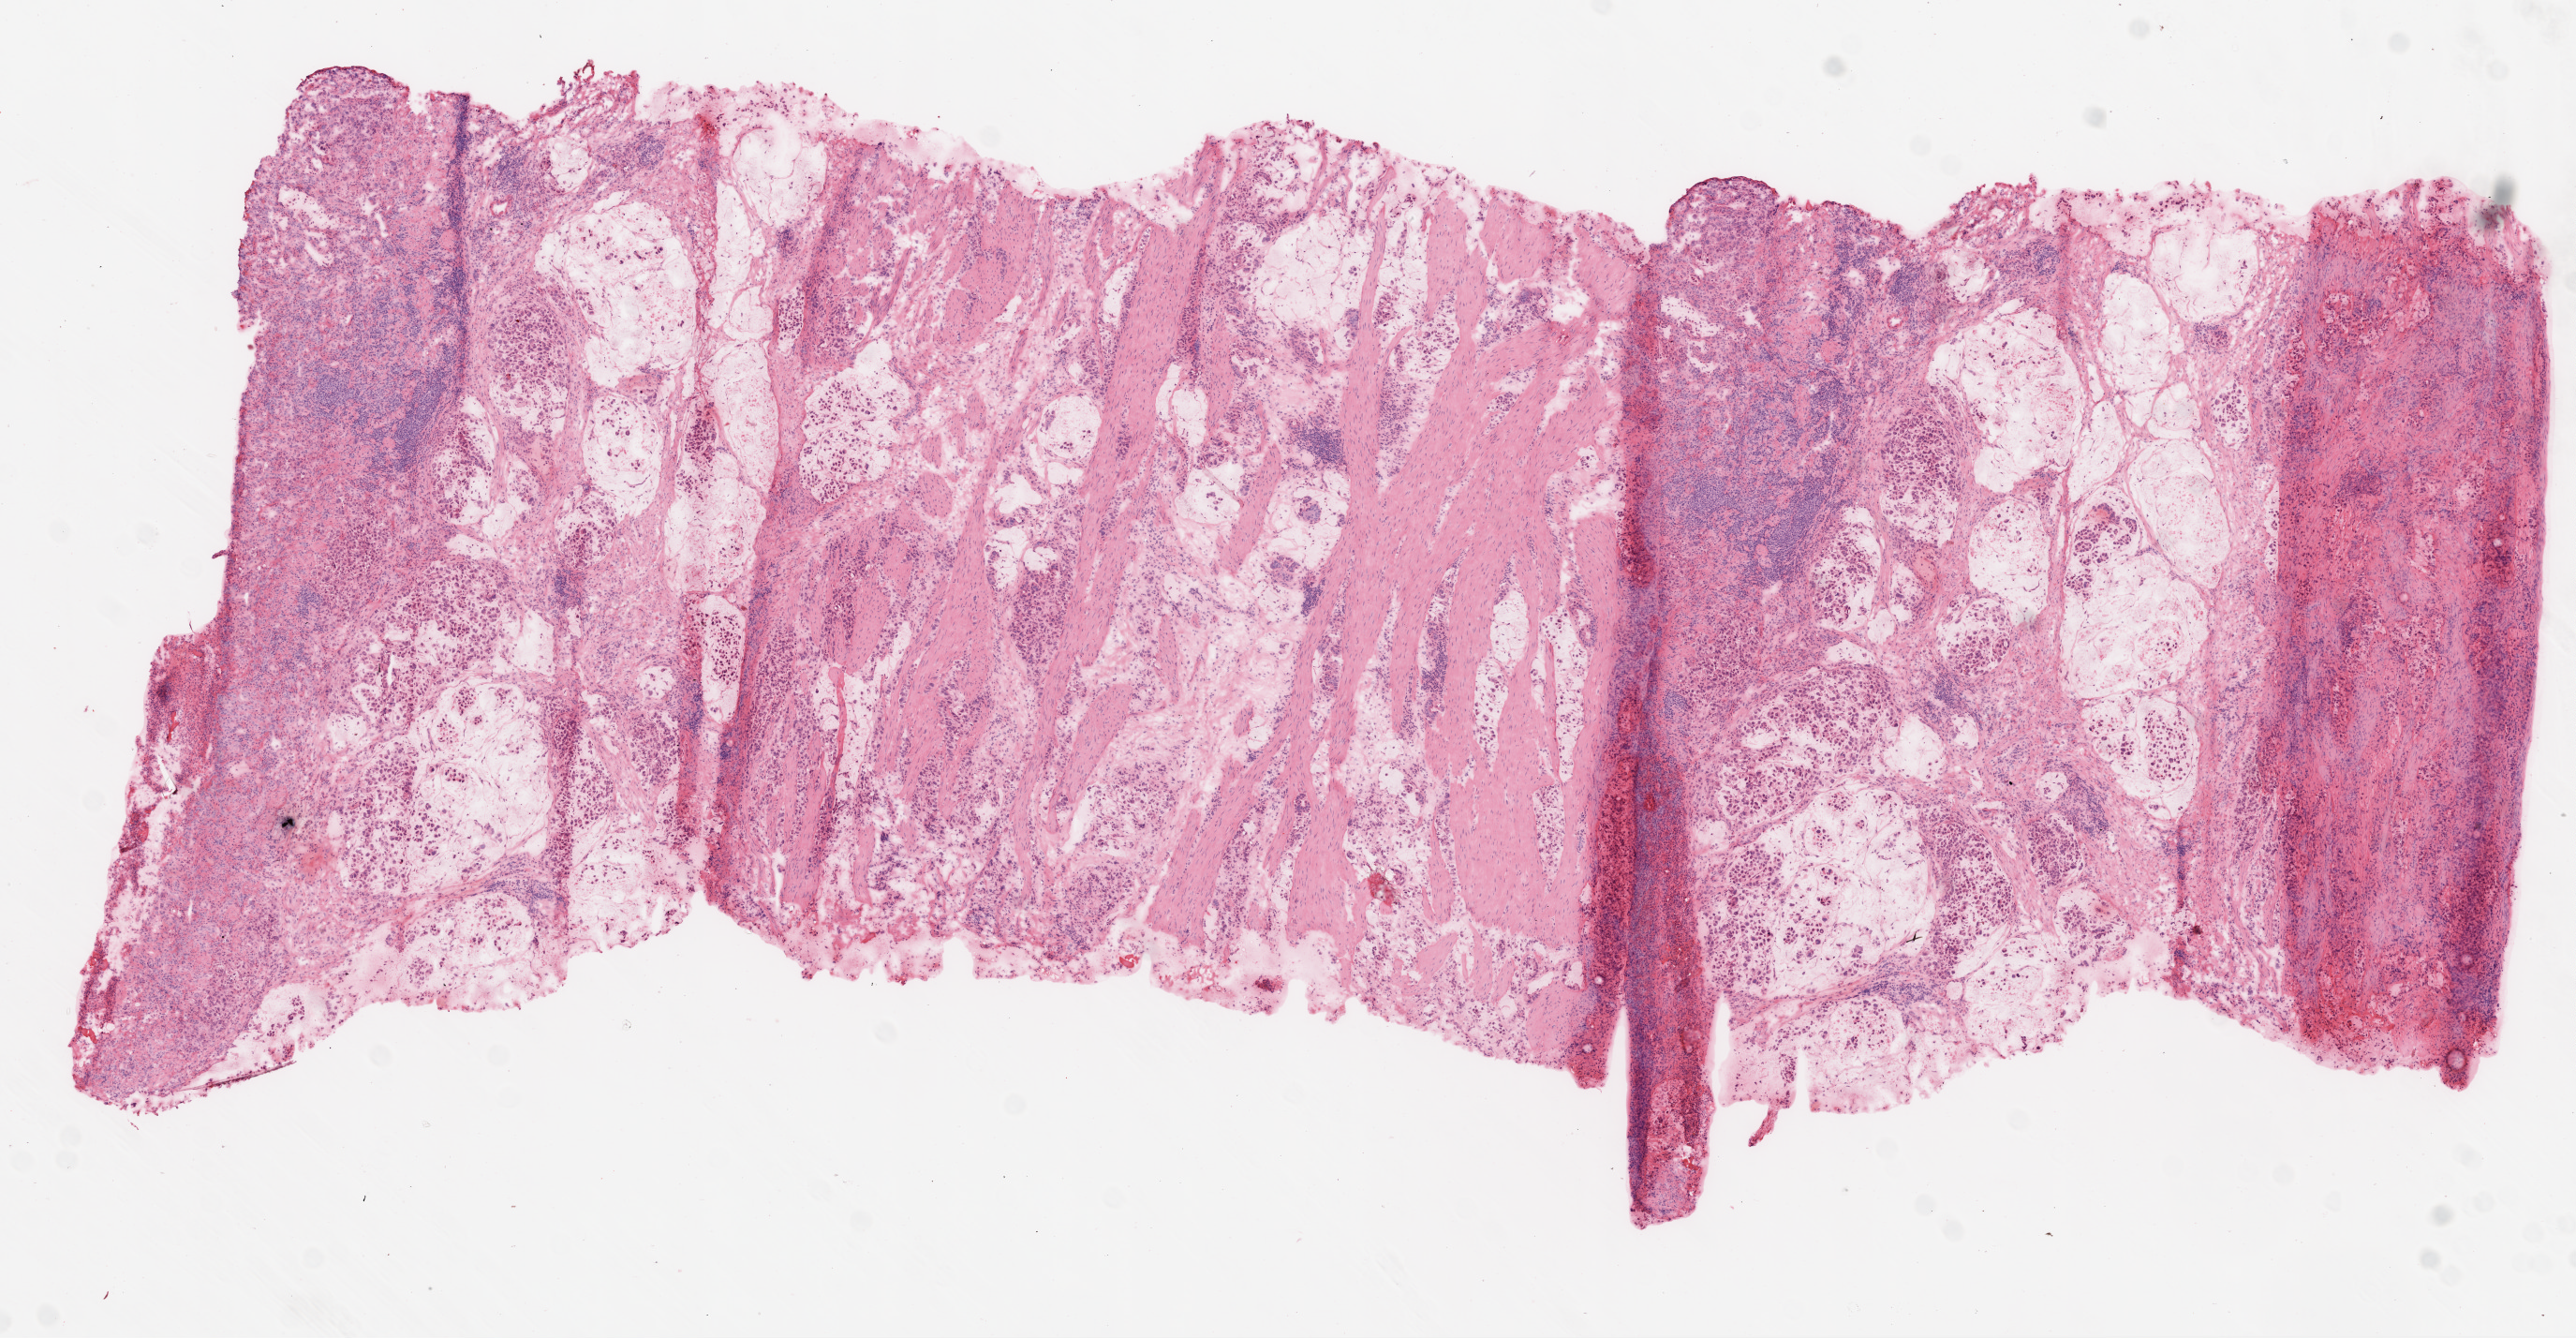
H&E-stained whole-slide image, whole scanned area (about 11.0 x 5.7 mm, acquisition: 20x scan) shown as a low-resolution overview, frozen section from the top of the tissue portion, stomach, primary tumour sample. Male patient; age at initial diagnosis 74 years. Histologic grade: G3 (poorly differentiated). Pathologist review of this section (percent, as recorded): tumour cells 70%, tumour nuclei 75%, normal cells 0%, stromal cells 25%, necrosis 5%.
TNM: T3 N2 M0. AJCC pathologic stage: IIIA. Histologic diagnosis: Mucinous adenocarcinoma.